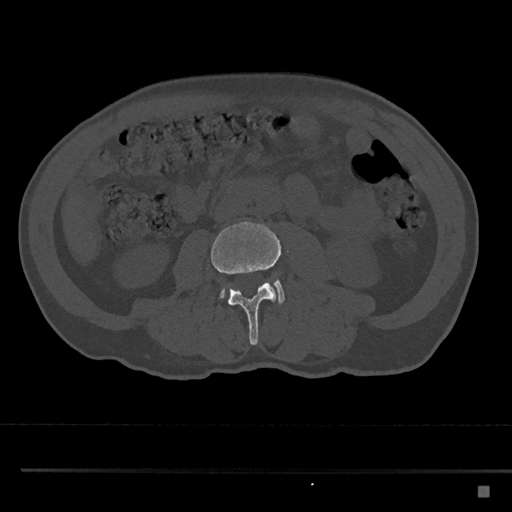
CT including the spine, one axial slice. Slice 683 of 797 in the series (ordered by position). Bone window (W 1800 / L 400 HU). 0.5 mm slice thickness. 512 × 512 image matrix, field of view 391 × 391 mm. Patient: male, 59 years. Case-level facts recorded for this patient, not image findings: primary cancer: prostate.
Structures marked on this image (semi-automatic segmentation, software-assisted and operator-edited):
- L3 vertebra: bounding box (x1, y1, x2, y2) in pixels: (210, 221, 283, 345)
- L4 vertebra: (219, 279, 285, 304)